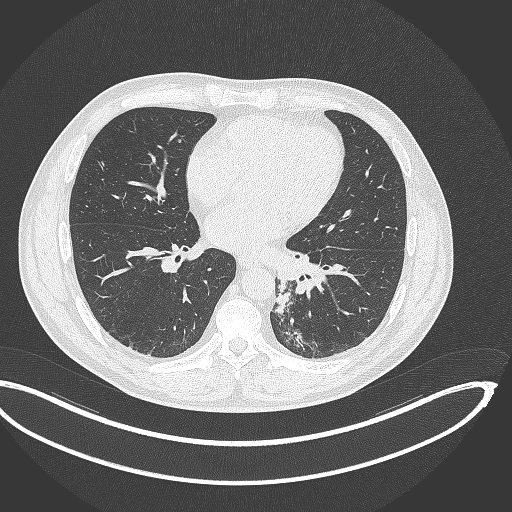
Chest CT, one axial slice; position 151 of 362 along the scan axis; 120 kVp; lung window (W 1500 / L -600 HU); 512 × 512 image matrix, field of view 442 × 442 mm. Male patient, age 50 years. Case-level facts recorded for this patient, not image findings: clinical TNM (as recorded): T2a N3 M0.
Structures marked on this image (bounding box drawn by a radiologist):
- lung tumour (recorded histology: squamous cell carcinoma): box from (x=275, y=285) to (x=294, y=316) px